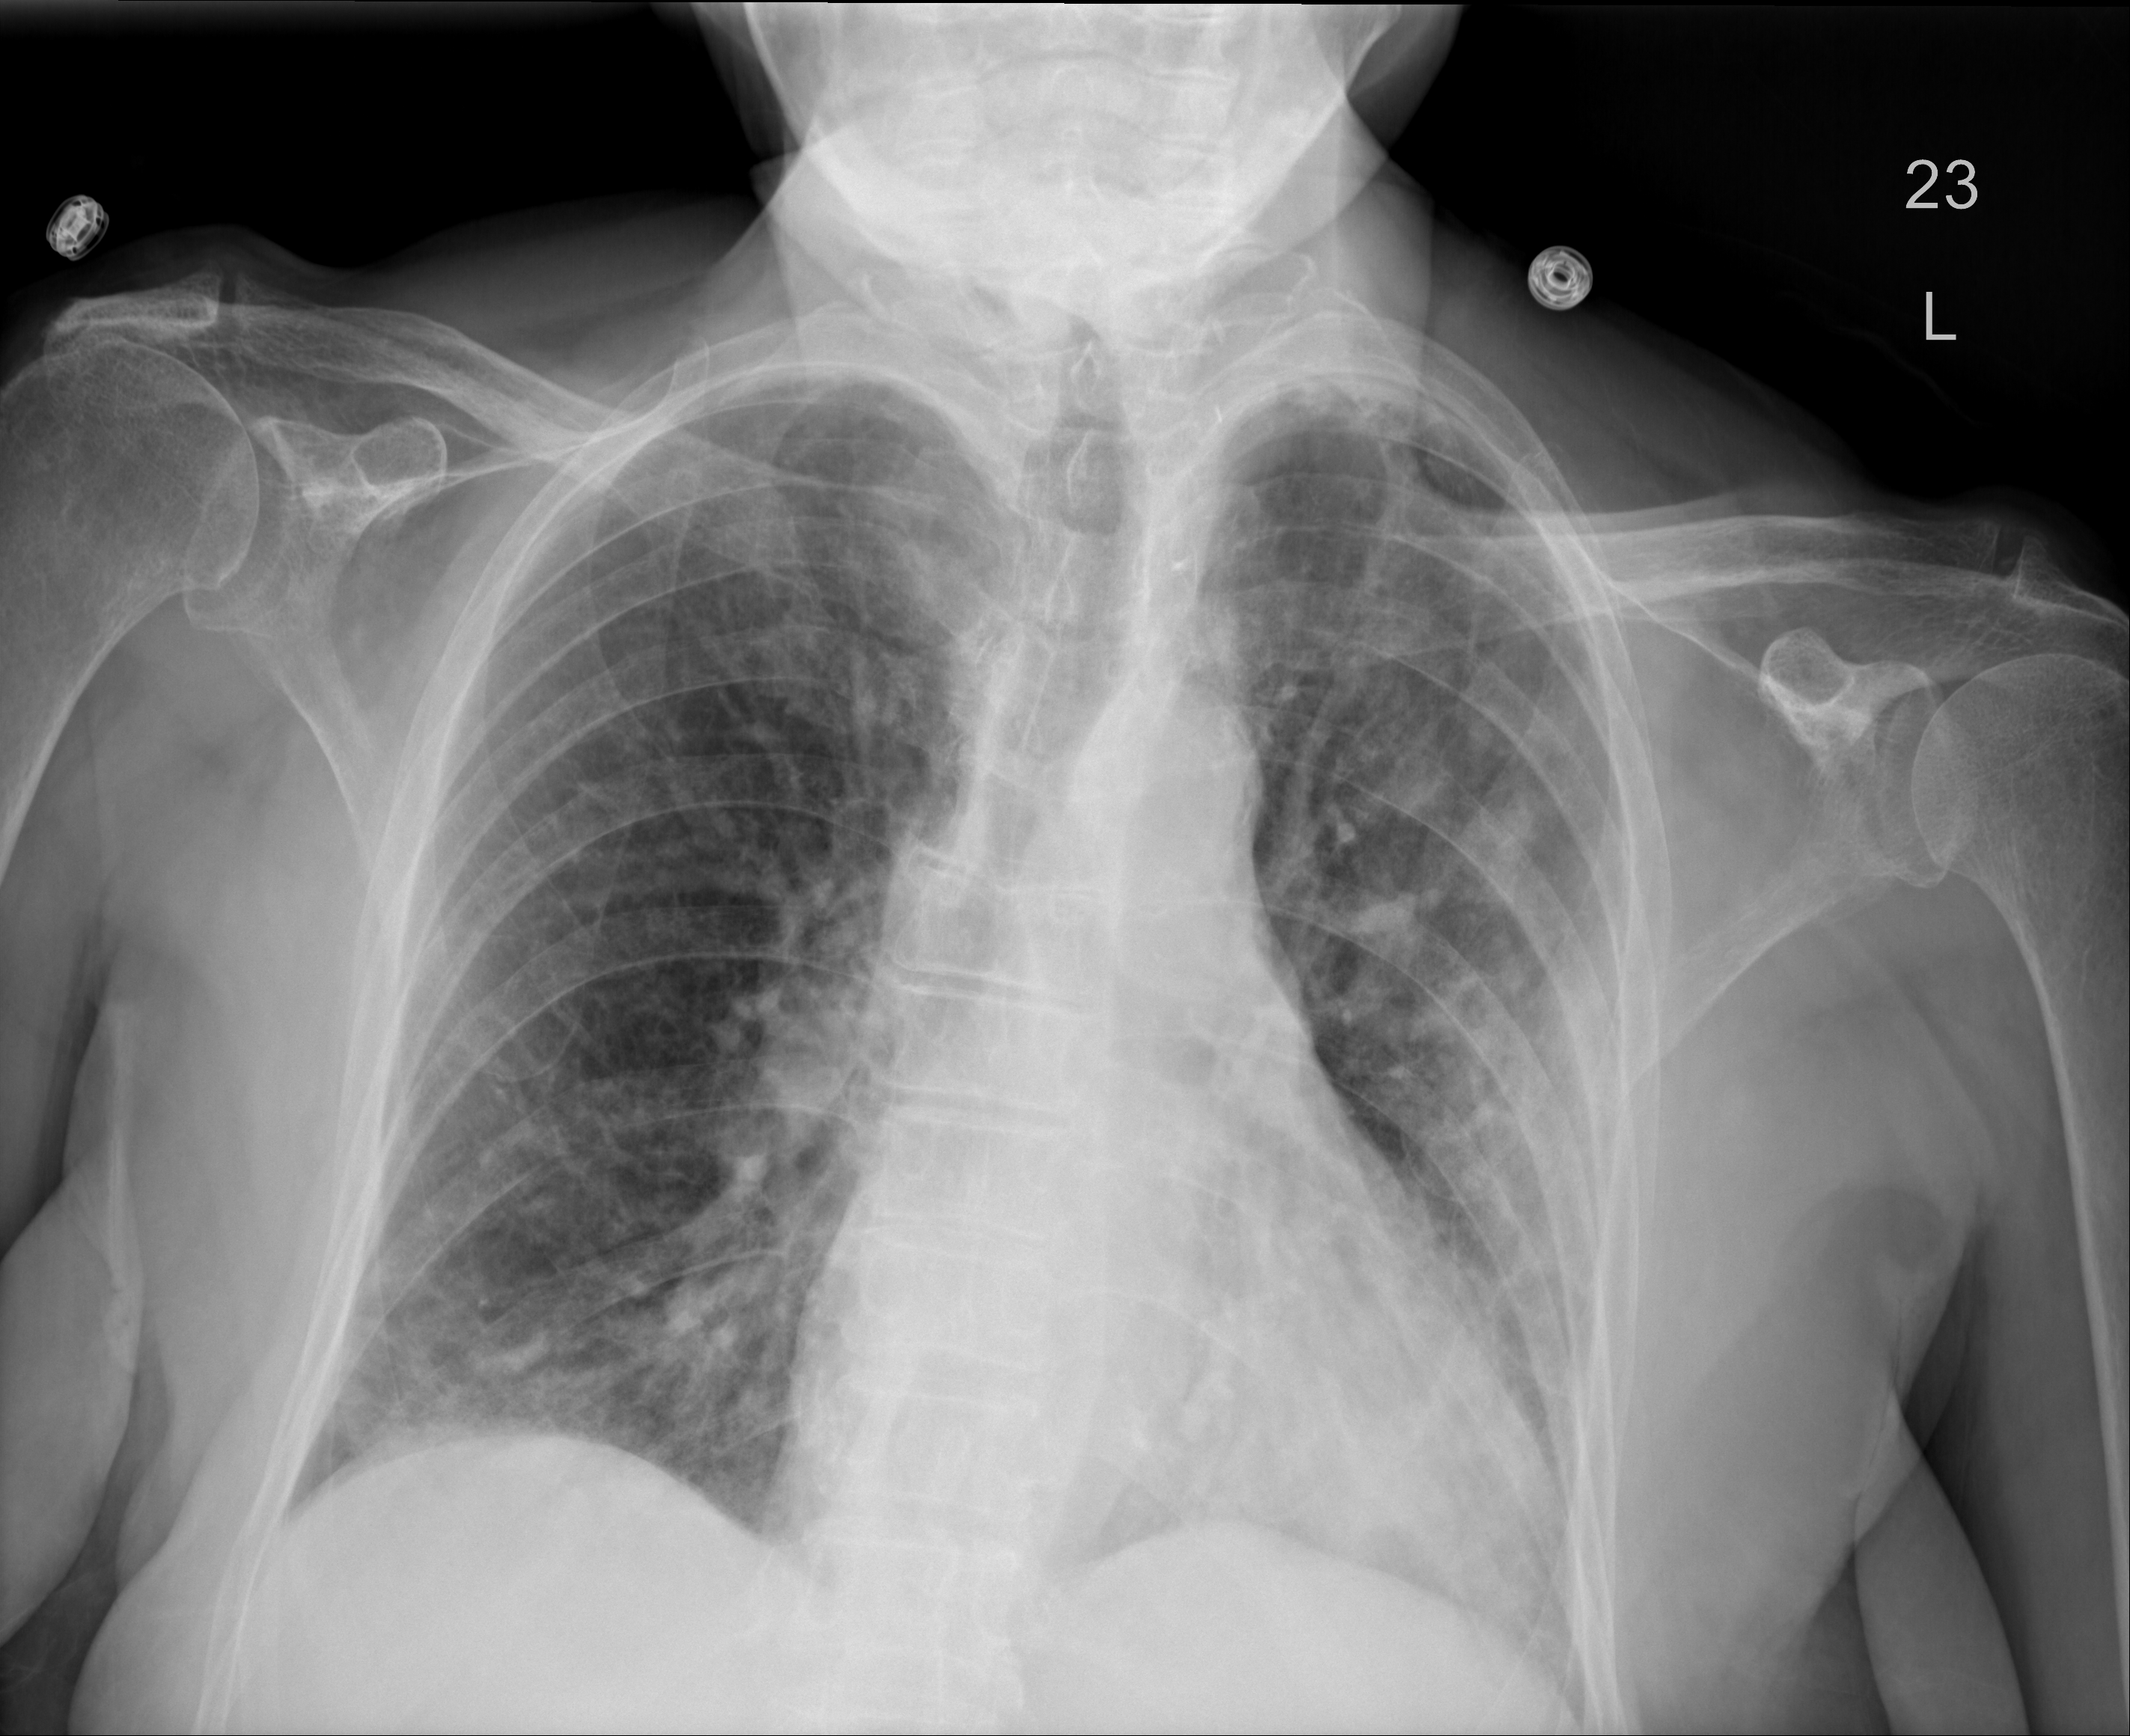
Chest X-ray, lateral projection. Female patient, age 75 years; imaged 2 days after the COVID-19 diagnosis.
Radiologist's key findings for this exam: Patchy ground-glass changes are seen within the left lung and in the right lower lung not significantly changed compared to the prior study.